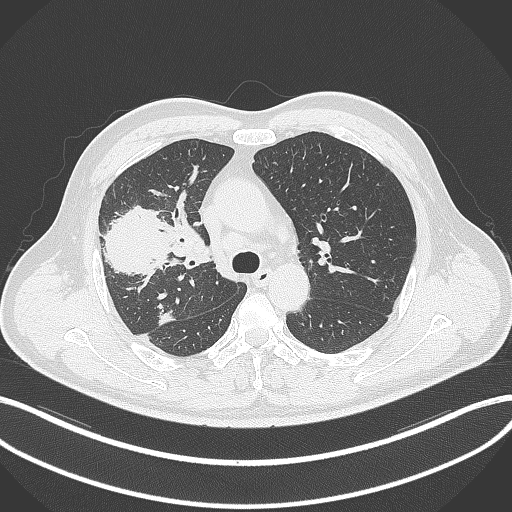
Chest CT, one axial slice. Slice 225 of 348 in the series (ordered by position). Lung window (W 1500 / L -600 HU). 512 × 512 image matrix, field of view 400 × 400 mm. Patient: male, 55 years. From the clinical record (not read from this slice): clinical TNM (as recorded): T3 N2 M1.
Annotated regions visible in this slice (bounding box drawn by a radiologist):
- lung tumour (recorded histology: adenocarcinoma): box from (x=100, y=205) to (x=173, y=279) px